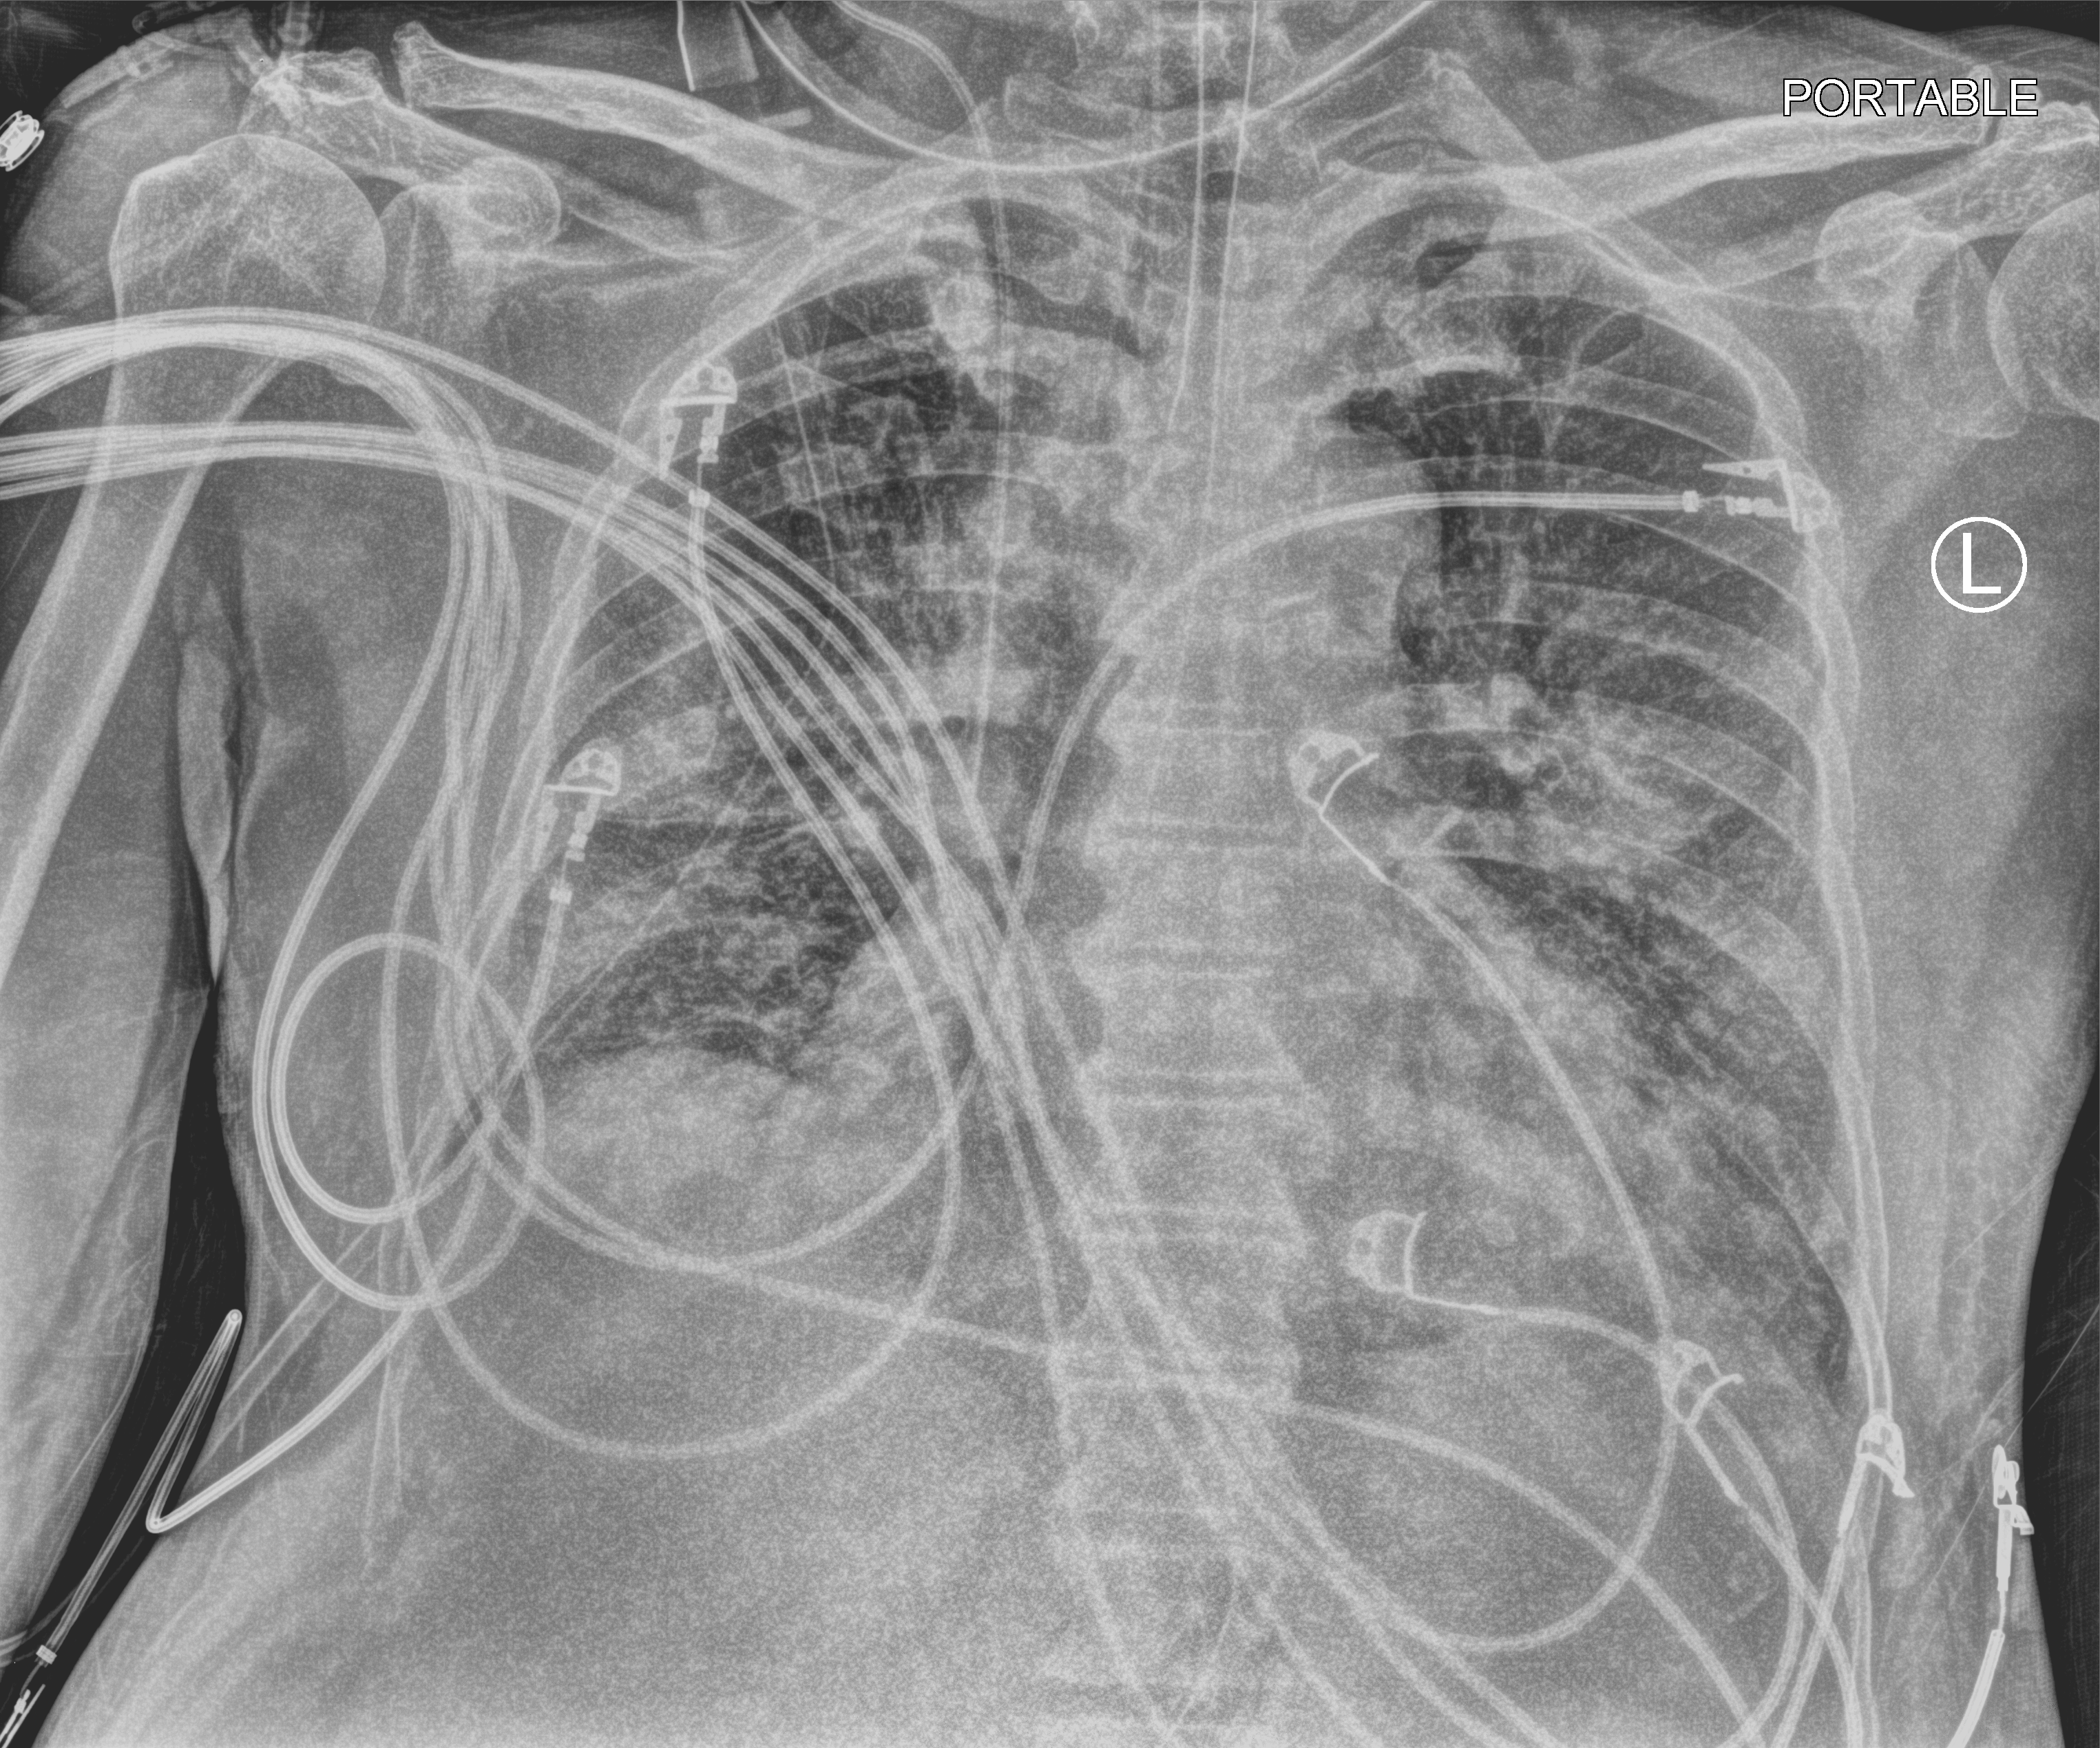
Chest X-ray (portable), anteroposterior (AP) projection. Patient hospitalised with COVID-19; male, aged 60–74 years.
Admission-level facts for this patient (not findings on this image; timing relative to this image not recorded): mechanically ventilated during this hospital stay: yes; diabetes (admission record): no; chronic kidney disease (admission record): no.